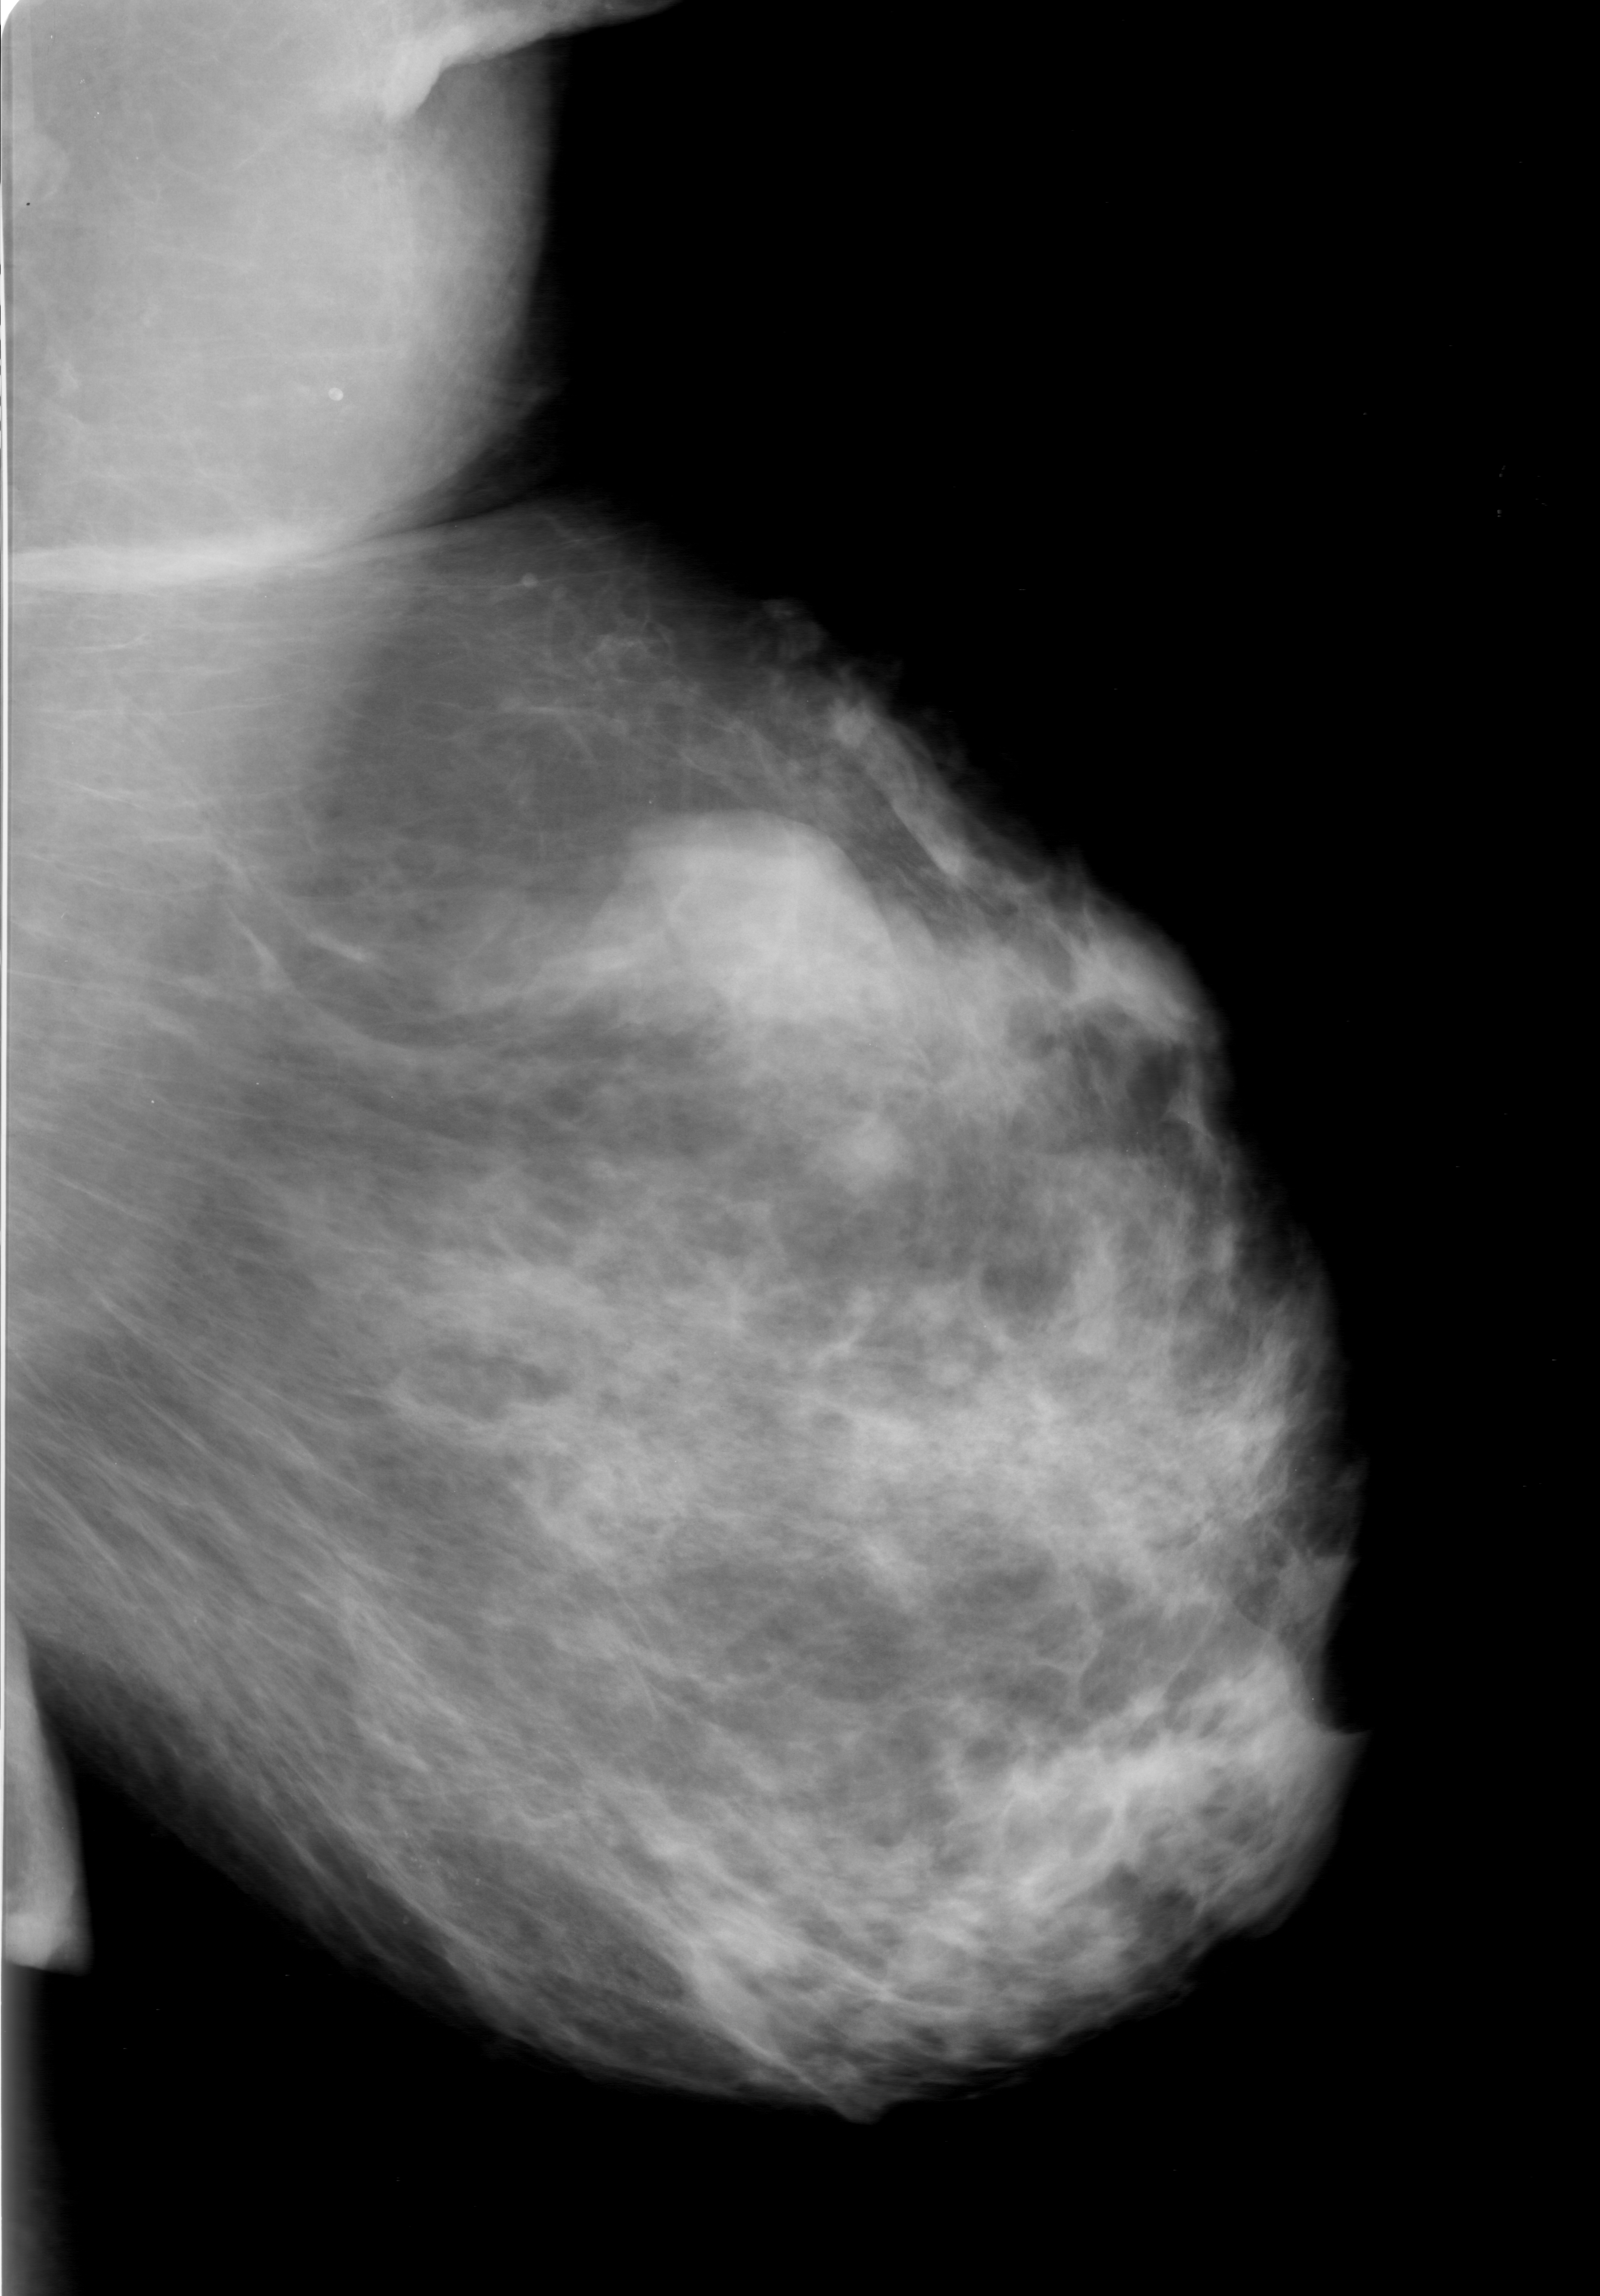
Scanned film-screen mammogram. Left breast. MLO view. BI-RADS breast density category 3 (scale 1–4). 1600 × 2296 image matrix.
Expert-marked regions of interest on this image (one box per marked abnormality):
- calcifications, morphology punctate / fine linear branching, distribution clustered; BI-RADS assessment category 0 (incomplete: needs additional imaging); subtlety rating 4 on a 1 (subtle) to 5 (obvious) scale; pathology result (as recorded, not read from the image): malignant: box from (x=276, y=1793) to (x=512, y=1992) px